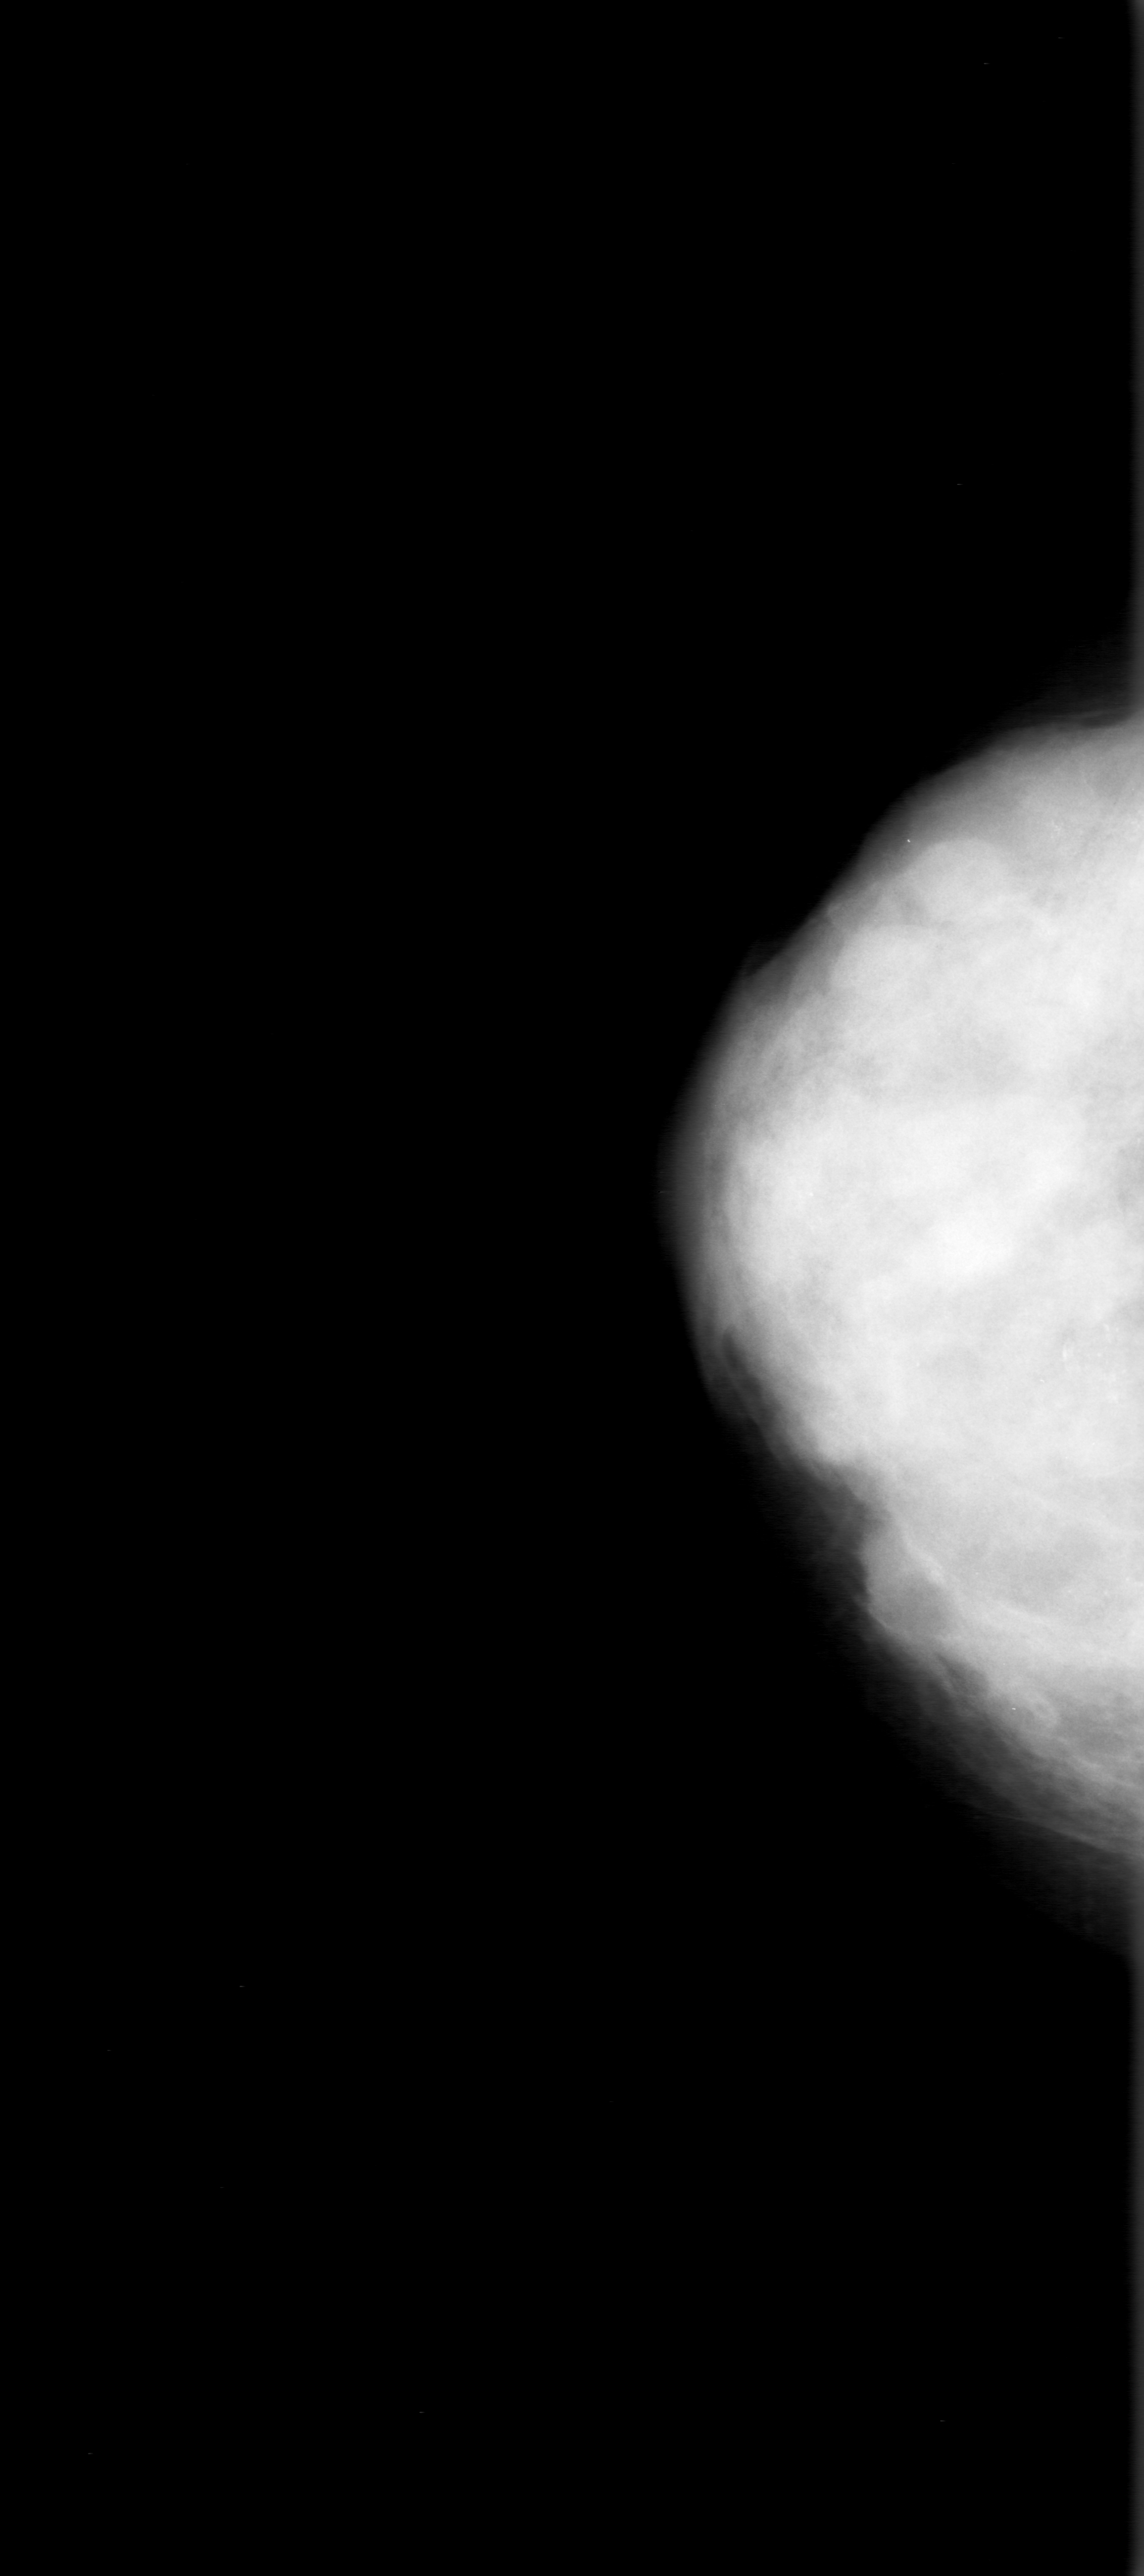
Scanned film-screen mammogram; right breast; craniocaudal (CC) view; BI-RADS breast density category 4 (scale 1–4); 1144 × 2576 image matrix.
Expert-marked regions of interest on this film, with their recorded descriptors:
- calcifications, morphology pleomorphic, distribution segmental; BI-RADS assessment category 5; subtlety rating 5 on a 1 (subtle) to 5 (obvious) scale; pathology result (as recorded, not read from the image): malignant: bounding box <955,1092,1129,1600> (left, top, right, bottom; pixels)